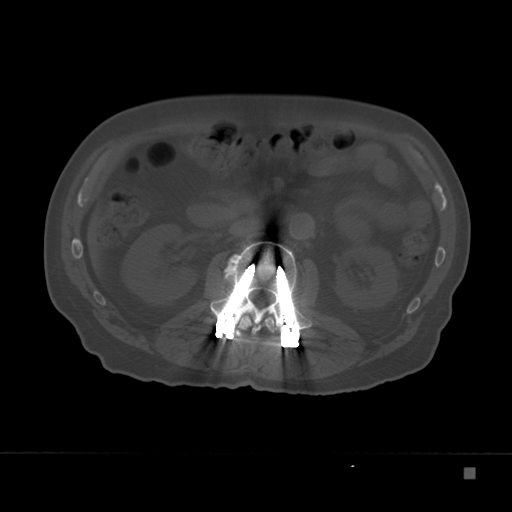
CT including the spine, one axial slice; reconstruction kernel Br40s; 120 kVp; bone window (W 1800 / L 400 HU); 512 × 512 image matrix, field of view 389 × 389 mm. Male patient, age 72 years. Case-level facts recorded for this patient, not image findings: primary cancer: skeletal.
Outlined on this slice (semi-automatic segmentation, software-assisted and operator-edited):
- L1 vertebra: bounding box <238,314,275,334> (left, top, right, bottom; pixels)
- L2 vertebra: <210,242,316,331>